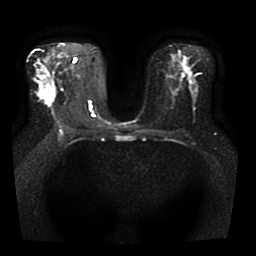
Breast MRI, one axial slice. Slice 24 of 41 in the series (ordered by position). Diffusion-weighted series; image 2 of 4 stored at this slice position (different b-values; order by instance number). 1.5 T. 5 mm slice thickness. 256 × 256 image matrix. Female patient.
Structures marked on this image (outlined manually by an expert reader):
- tumour on diffusion-weighted imaging: box from (x=42, y=92) to (x=52, y=103) px